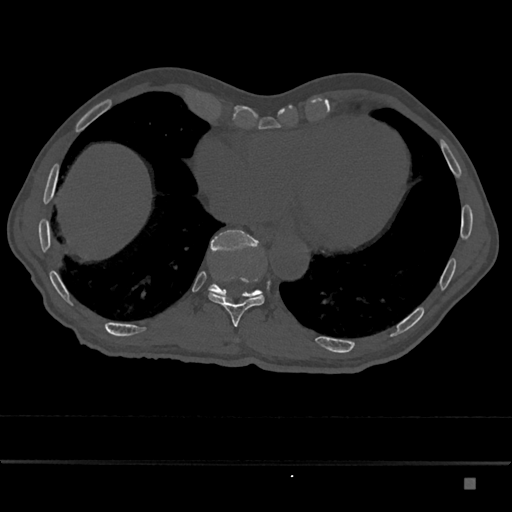
CT including the spine, one axial slice. Position 725 of 797 along the scan axis. Bone window (W 1800 / L 400 HU). 512 × 512 image matrix. Male patient, age 72 years. From the clinical record (not read from this slice): primary cancer: prostate.
Annotated regions visible in this slice (semi-automatically segmented with operator editing):
- T10 vertebra: bounding box [x1, y1, x2, y2] px = [208, 278, 265, 327]
- T11 vertebra: [208, 230, 263, 299]